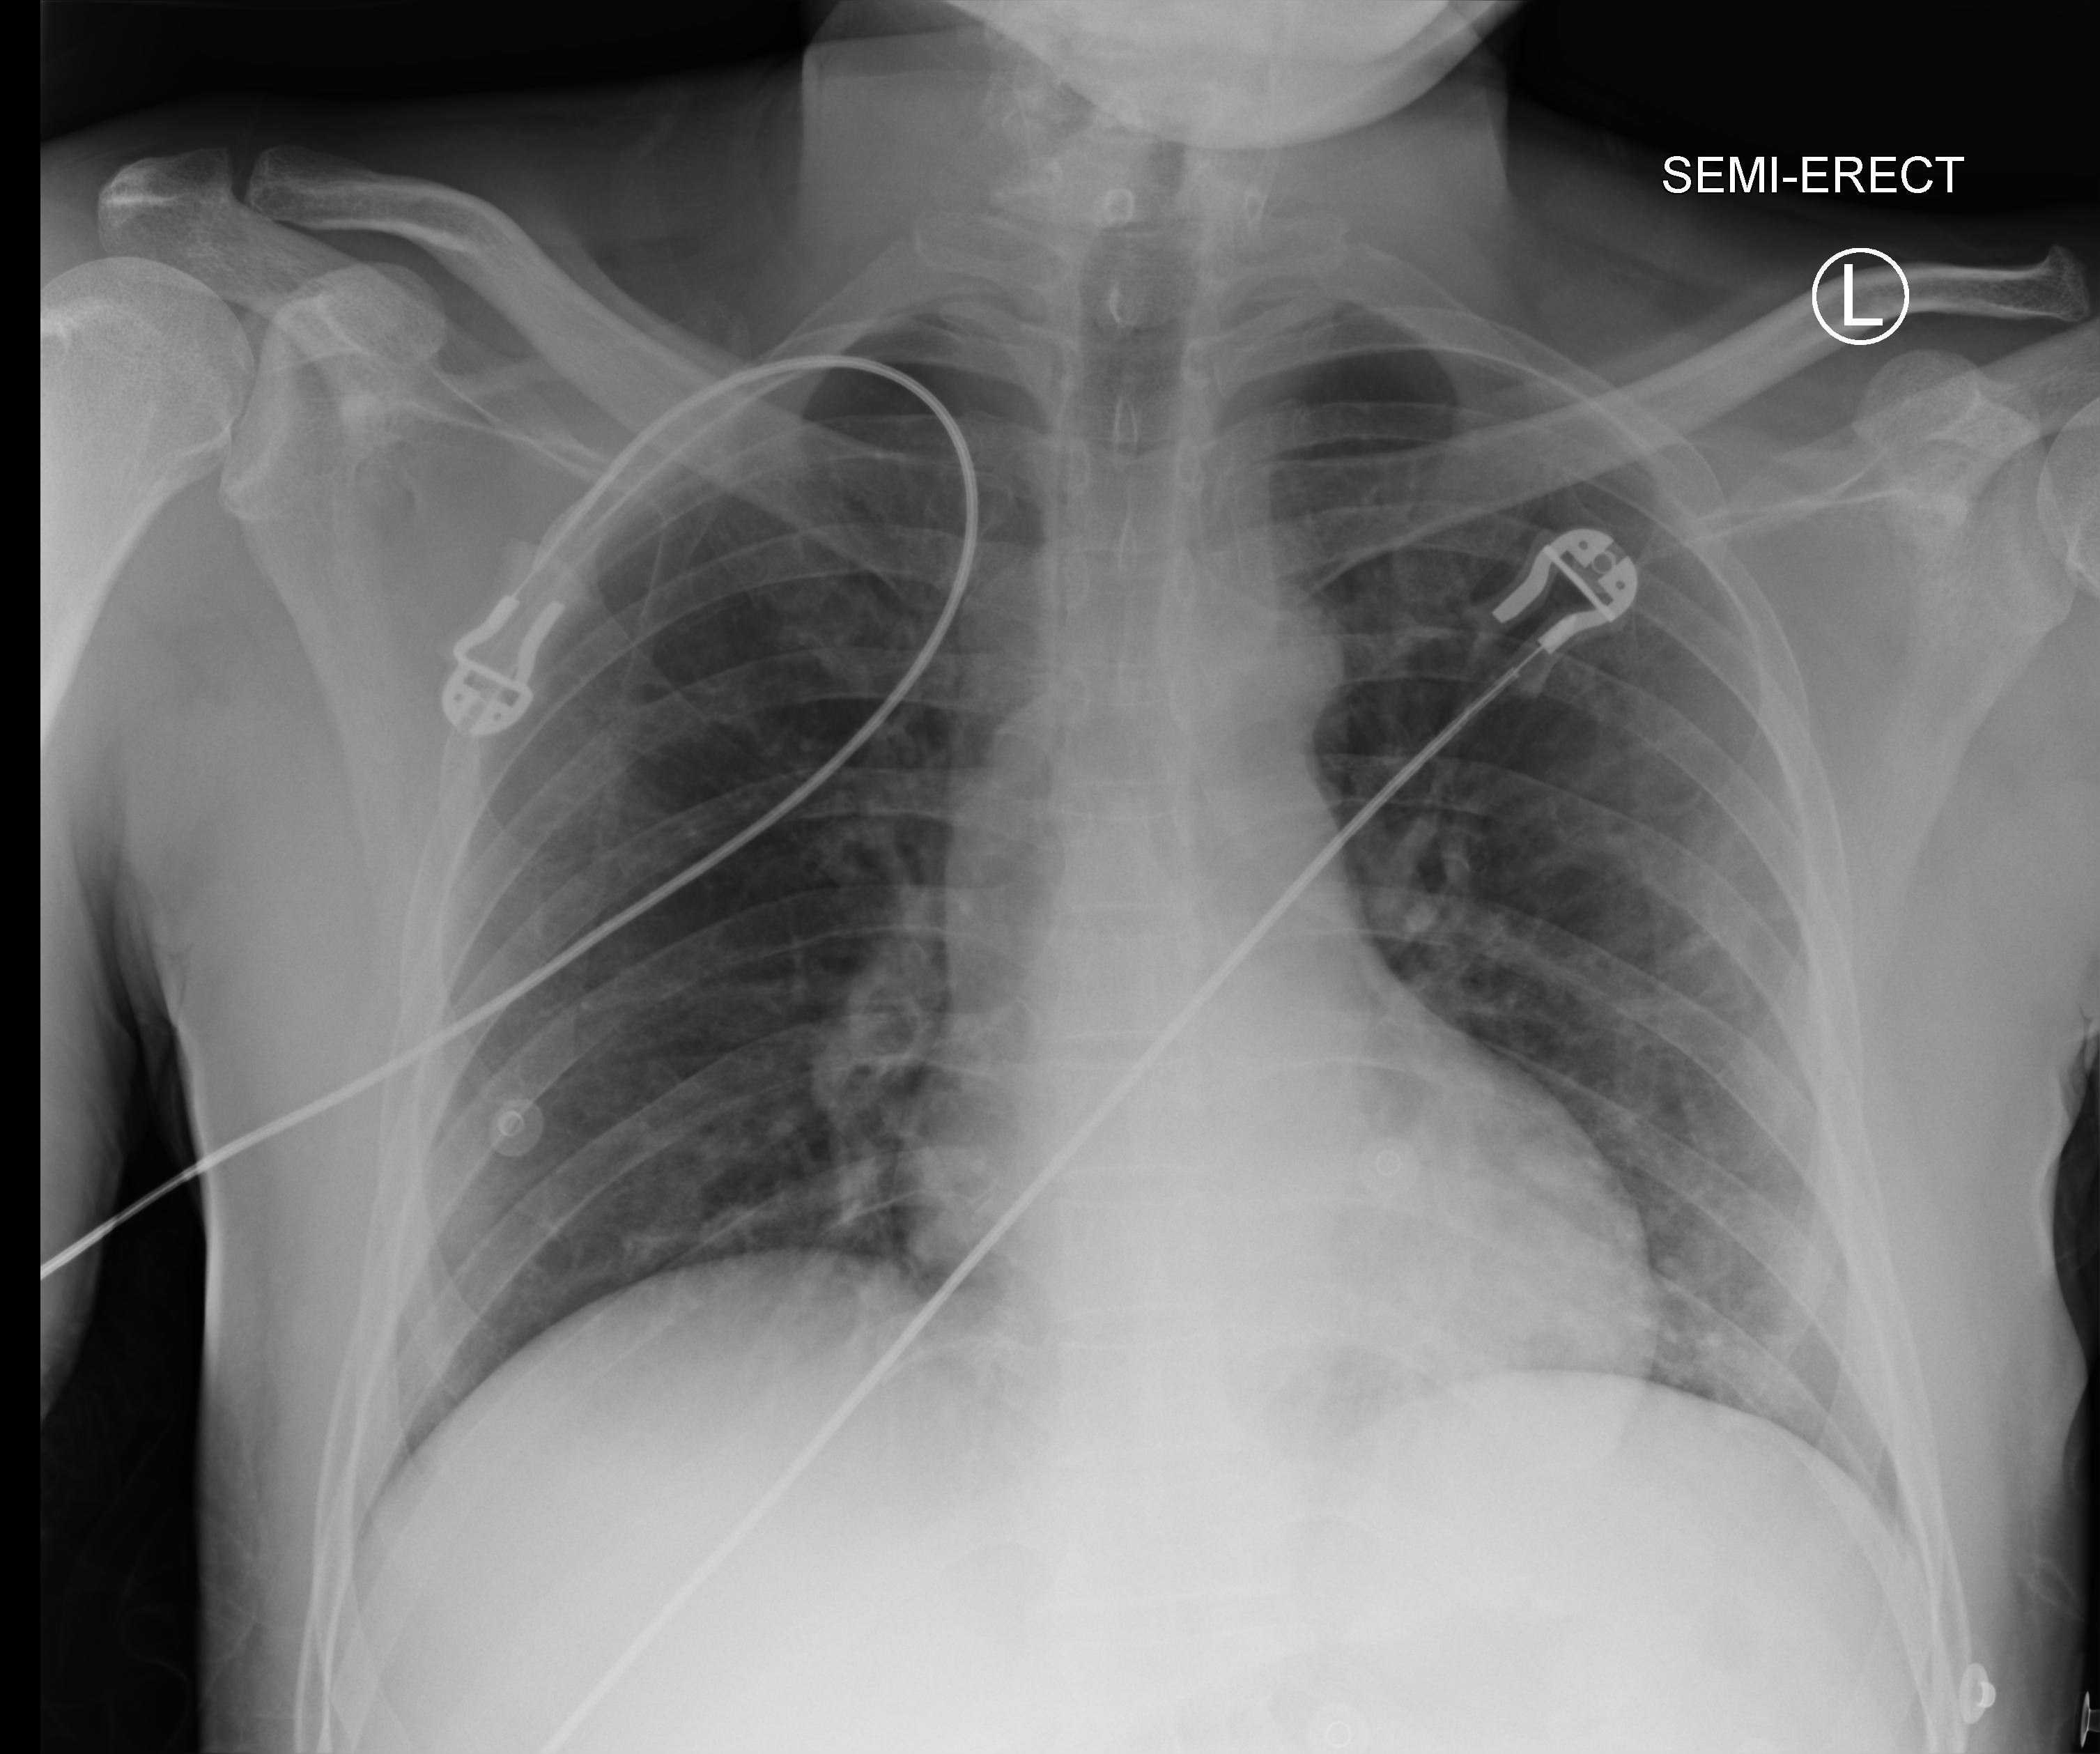
Chest X-ray (portable); anteroposterior (AP) projection. Patient hospitalised with COVID-19; male, aged 18–59 years.
Hospital-stay facts (about this admission, not read from this image; timing relative to this image not recorded): smoking status (admission record): never.